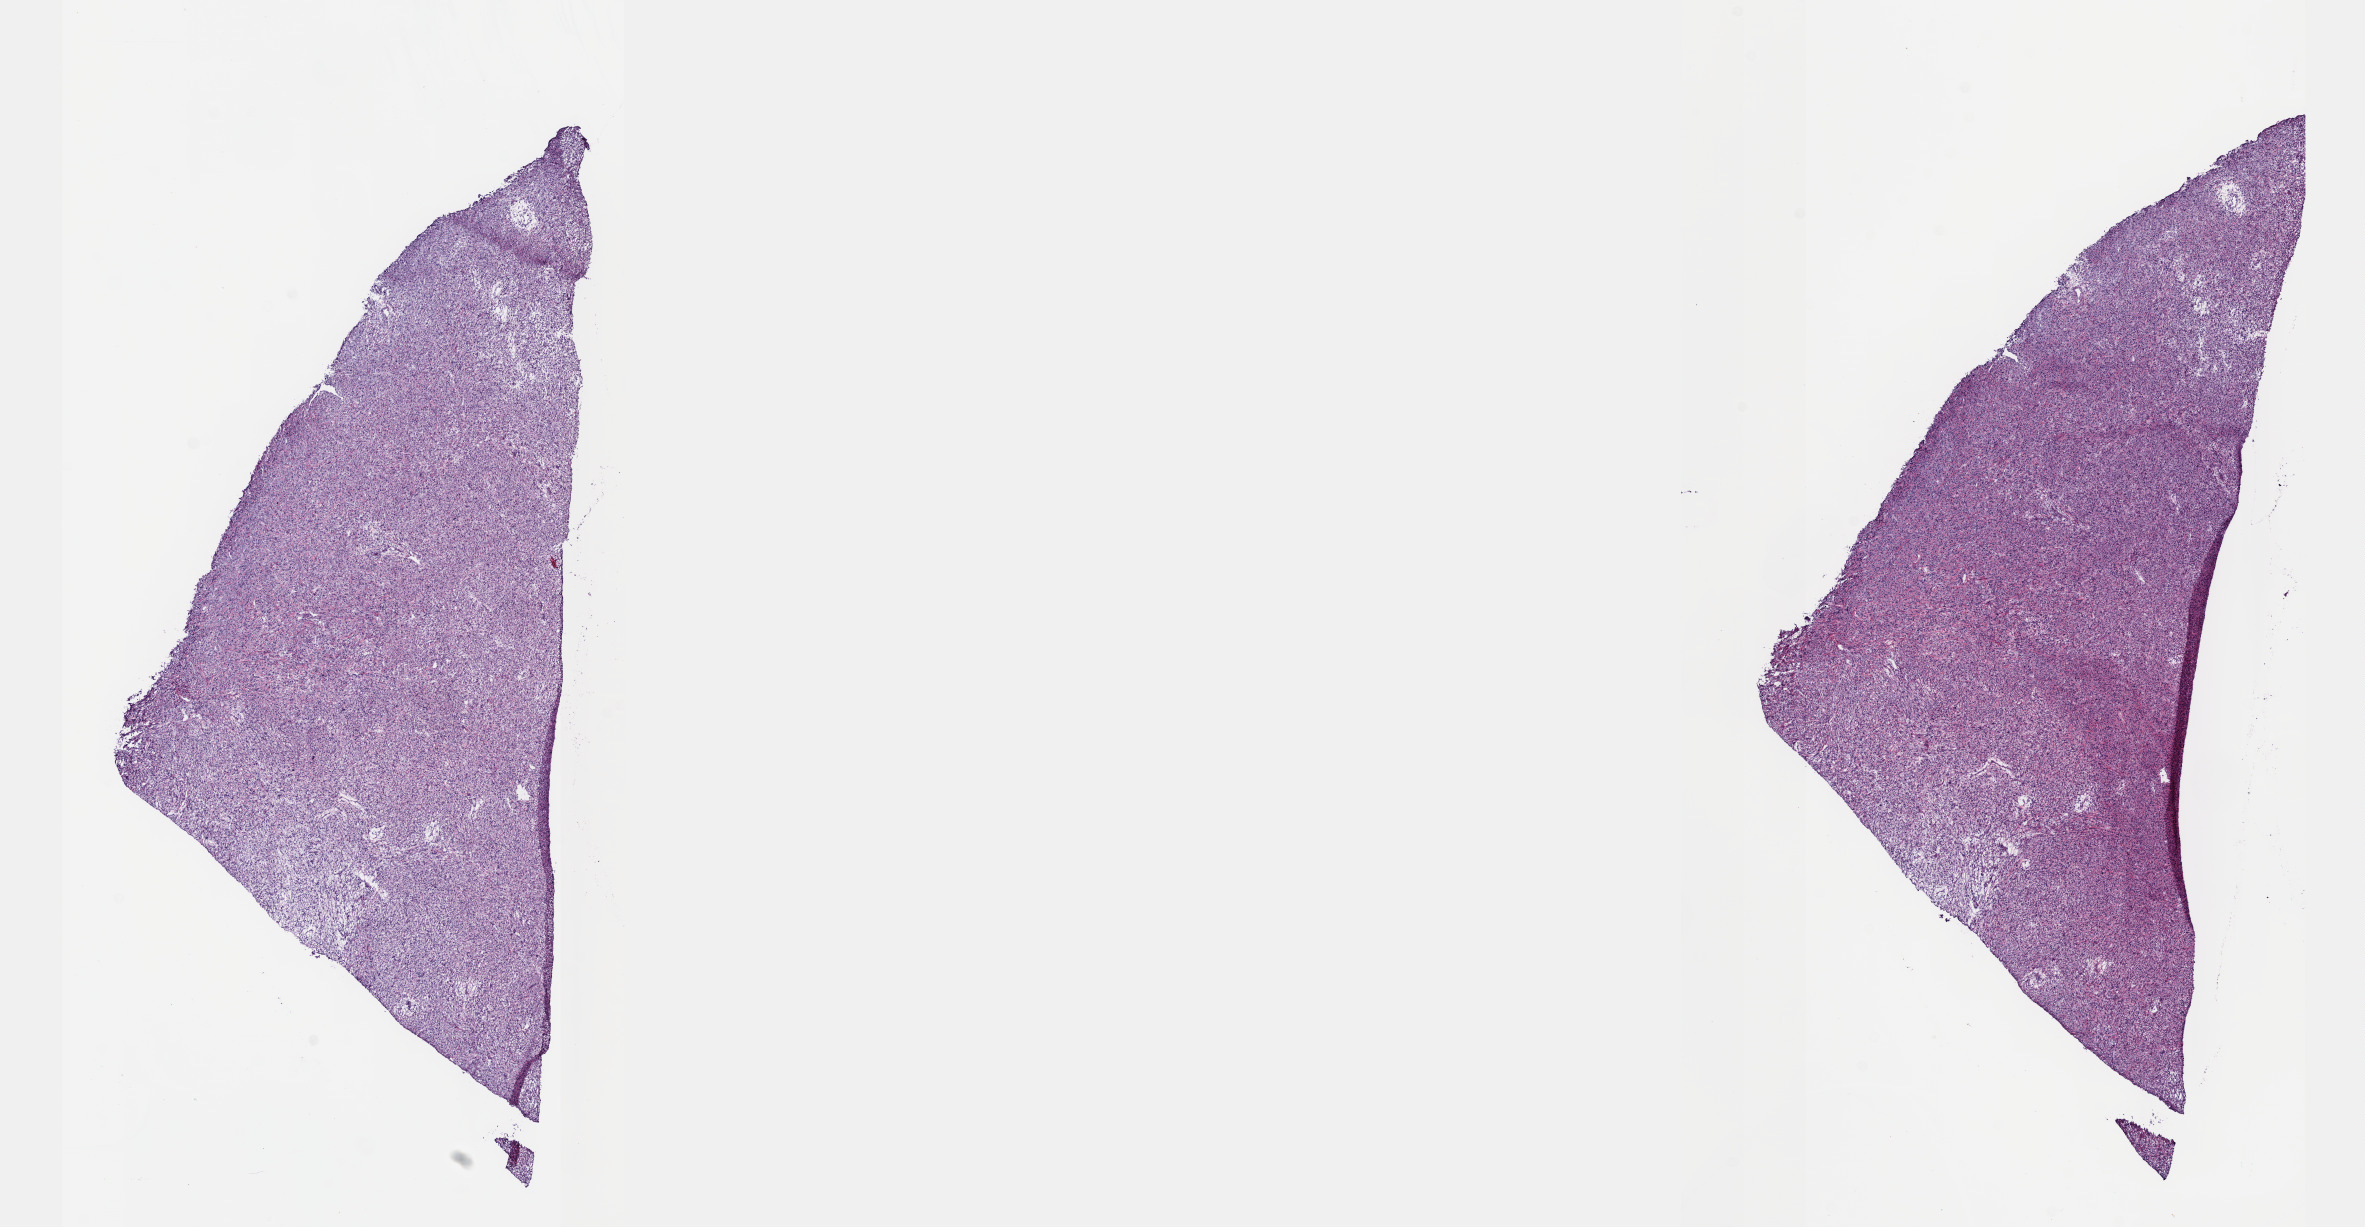
Digitized Hematoxylin and eosin (H&E) stained tissue section (whole slide) — whole scanned area (about 19.1 x 9.9 mm, acquisition: 40x scan) shown as a low-resolution overview. Frozen section. Sample: primary tumour, retroperitoneum and peritoneum. Patient: male, age at initial diagnosis 36 years. Slide review estimates, as recorded: tumour cells 85%, tumour nuclei 85%, normal cells 0%, stromal cells 14%, necrosis 1%. Infiltration values recorded for this section: lymphocyte infiltration 2%, monocyte infiltration 1%, neutrophil infiltration 2%.
- pathologic diagnosis: Dedifferentiated liposarcoma